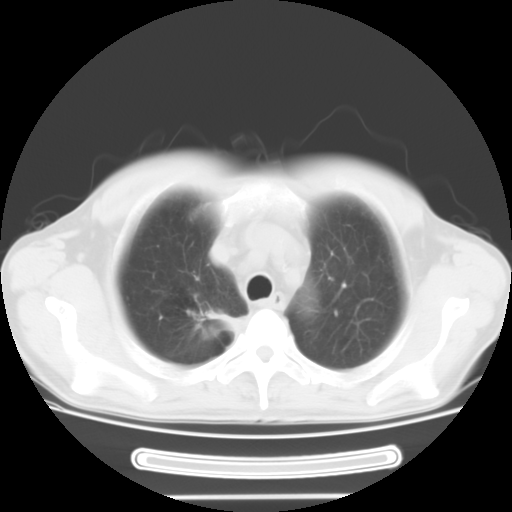
Chest CT, one axial slice. Slice 19 of 24 in the series (ordered by position). Reconstruction kernel STANDARD. Lung window (W 1500 / L -600 HU). 10 mm slice thickness. 512 × 512 image matrix, field of view 350 × 350 mm. Male patient, age 57 years. Case-level facts recorded for this patient, not image findings: clinical TNM (as recorded): T2 N3 M1b.
Annotated regions visible in this slice (bounding box drawn by a radiologist):
- lung tumour (recorded histology: adenocarcinoma): bounding box <205,306,242,330> (left, top, right, bottom; pixels)